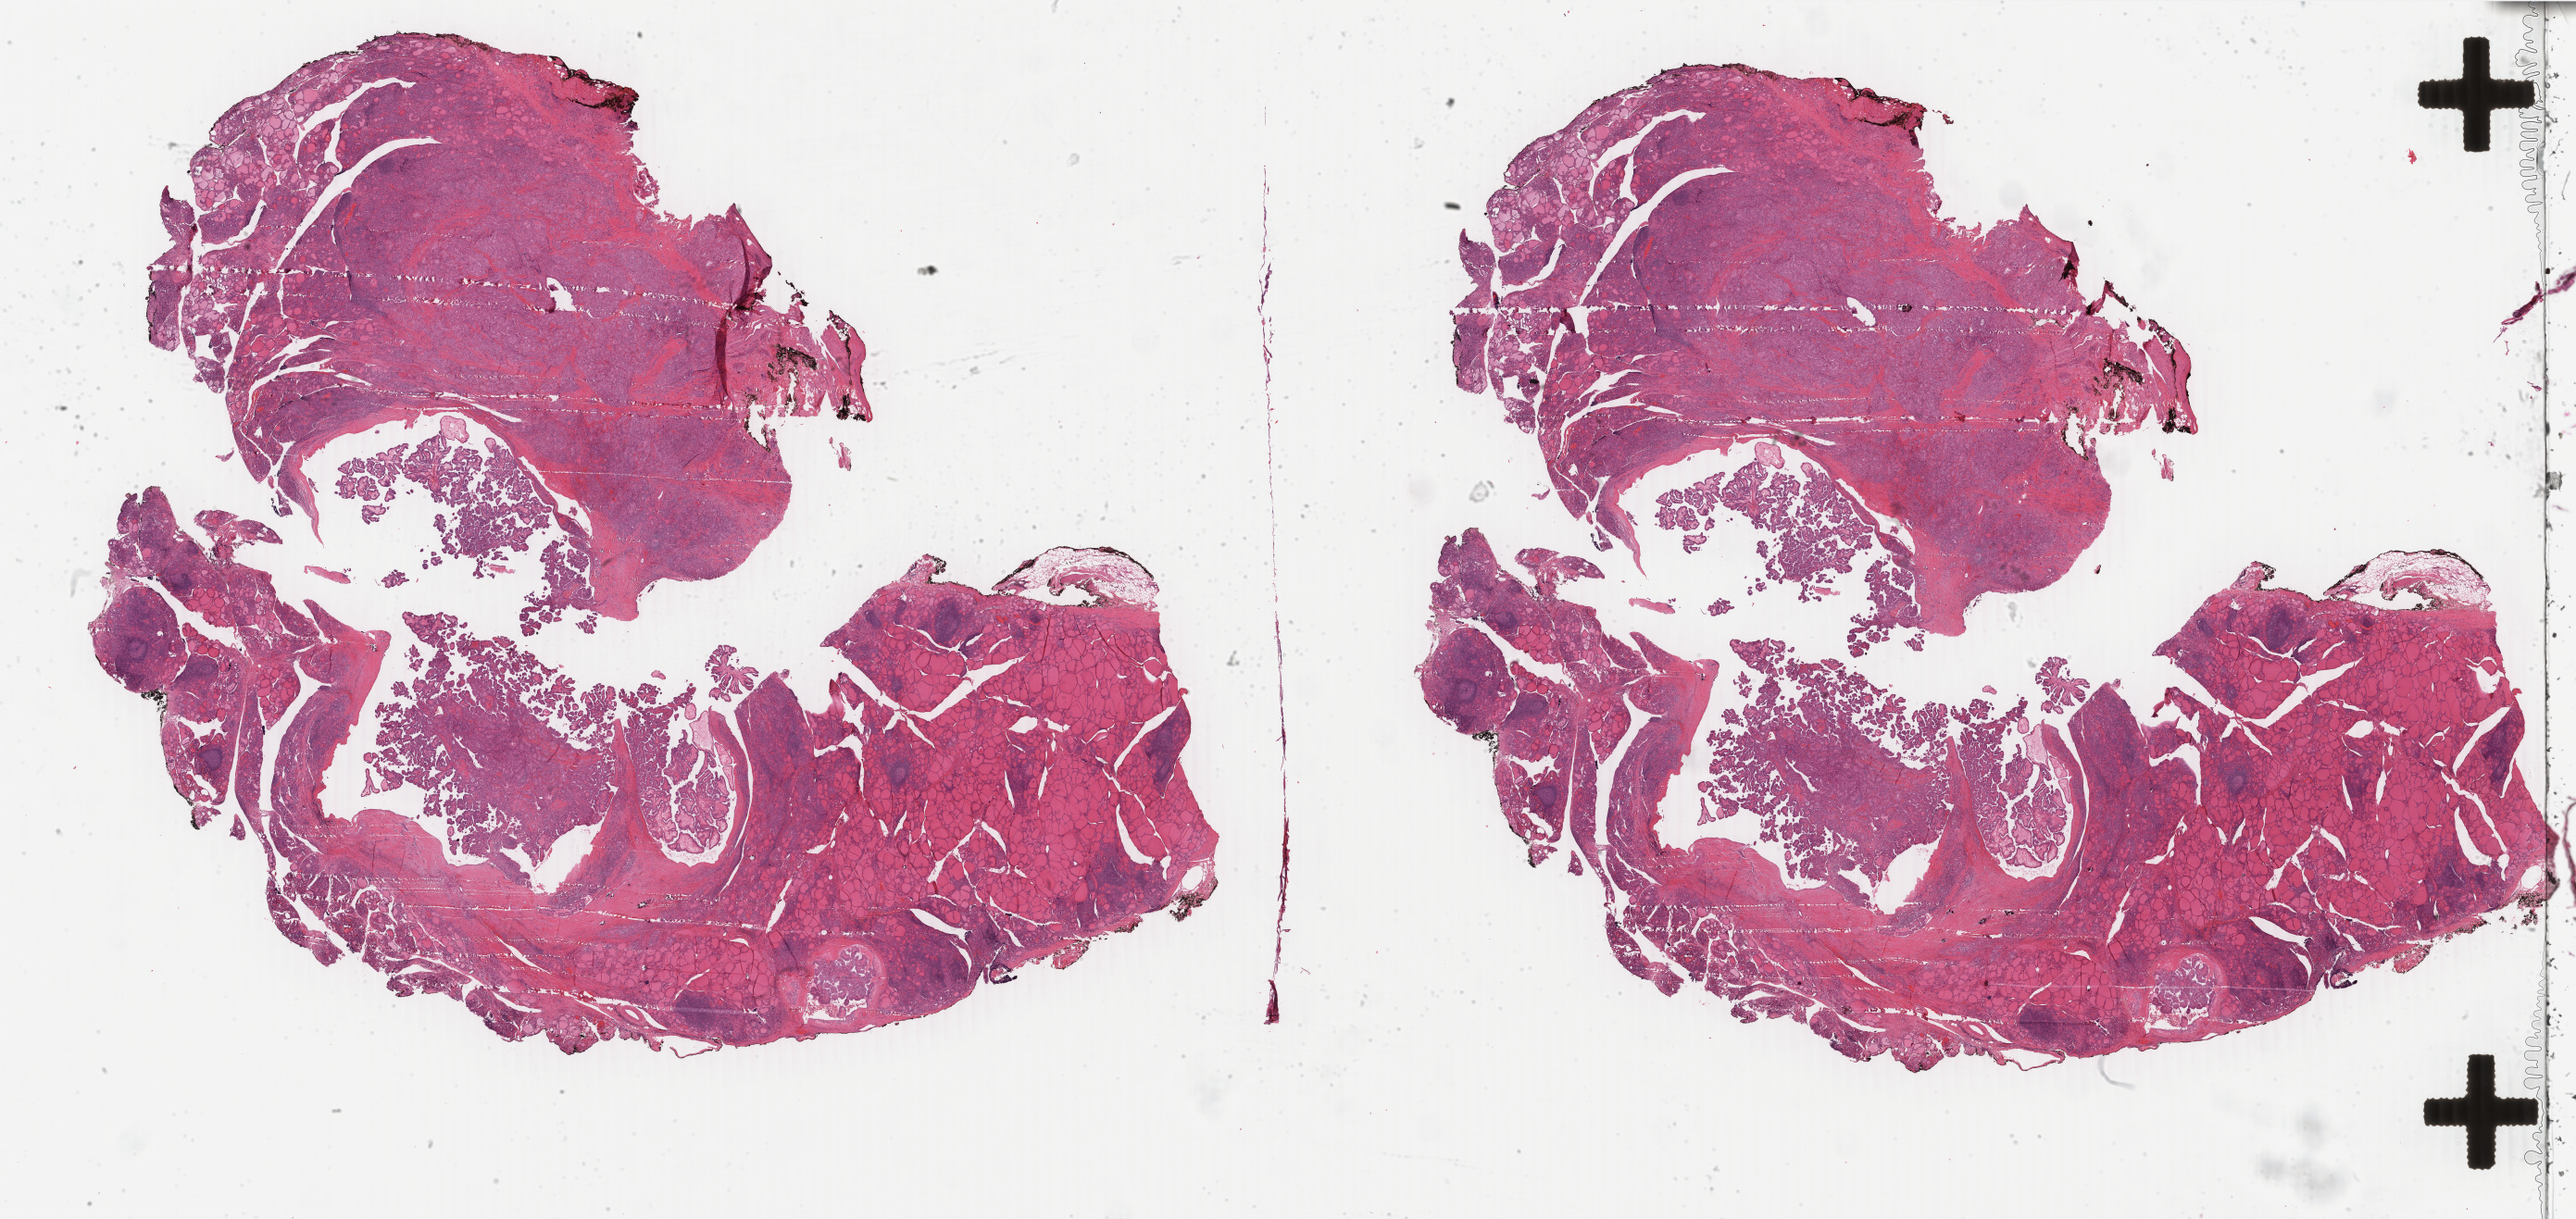
Digitized Hematoxylin and eosin (H&E) stained tissue section (whole slide), low-resolution overview of the scanned area, about 44.3 x 21.0 mm; formalin-fixed paraffin-embedded (FFPE) diagnostic section; thyroid, primary tumour sample. Patient: female, age at initial diagnosis 34 years.
* laterality: bilateral
* AJCC pathologic stage: I (7th edition)
* diagnosis: Papillary adenocarcinoma, NOS (thyroid gland)